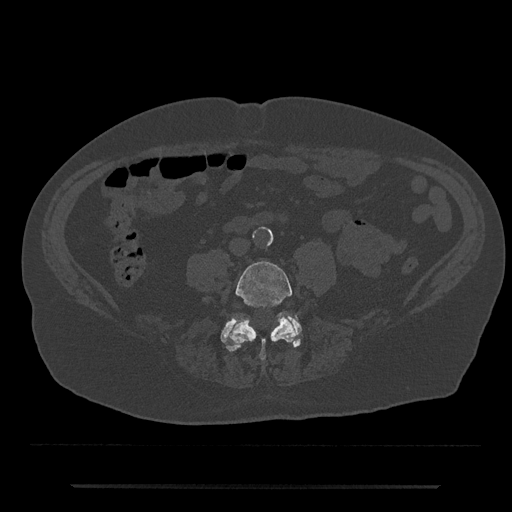
CT including the spine, one axial slice; position 334 of 797 along the scan axis; reconstruction kernel Br40s/3; 120 kVp; bone window (W 1800 / L 400 HU); 0.5 mm slice thickness; 512 × 512 image matrix. Patient: male, 80 years. From the clinical record (not read from this slice): primary cancer: prostate; vertebrae with lytic lesions (as recorded): L1, T11.
Annotated regions visible in this slice (semi-automatically segmented with operator editing):
- L4 vertebra: bounding box [x1, y1, x2, y2] px = [226, 261, 296, 360]
- L5 vertebra: [221, 314, 302, 352]